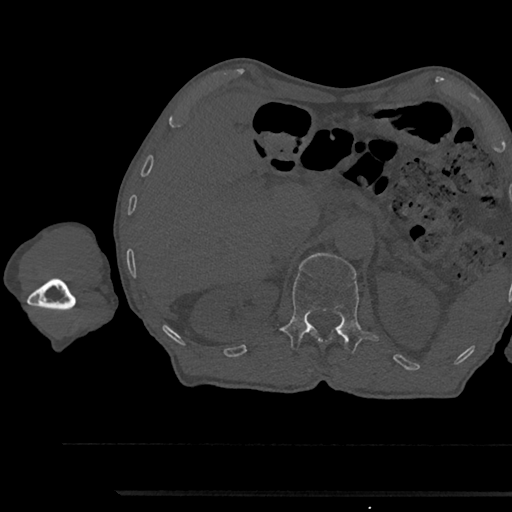
CT including the spine, one axial slice; position 660 of 797 along the scan axis; bone window (W 1800 / L 400 HU); 0.5 mm slice thickness; 512 × 512 image matrix, field of view 367 × 367 mm. Patient: male, 79 years. Case-level facts recorded for this patient, not image findings: primary cancer: prostate.
Structures marked on this image (semi-automatically segmented with operator editing):
- L1 vertebra: bounding box [x1, y1, x2, y2] px = [279, 253, 379, 353]